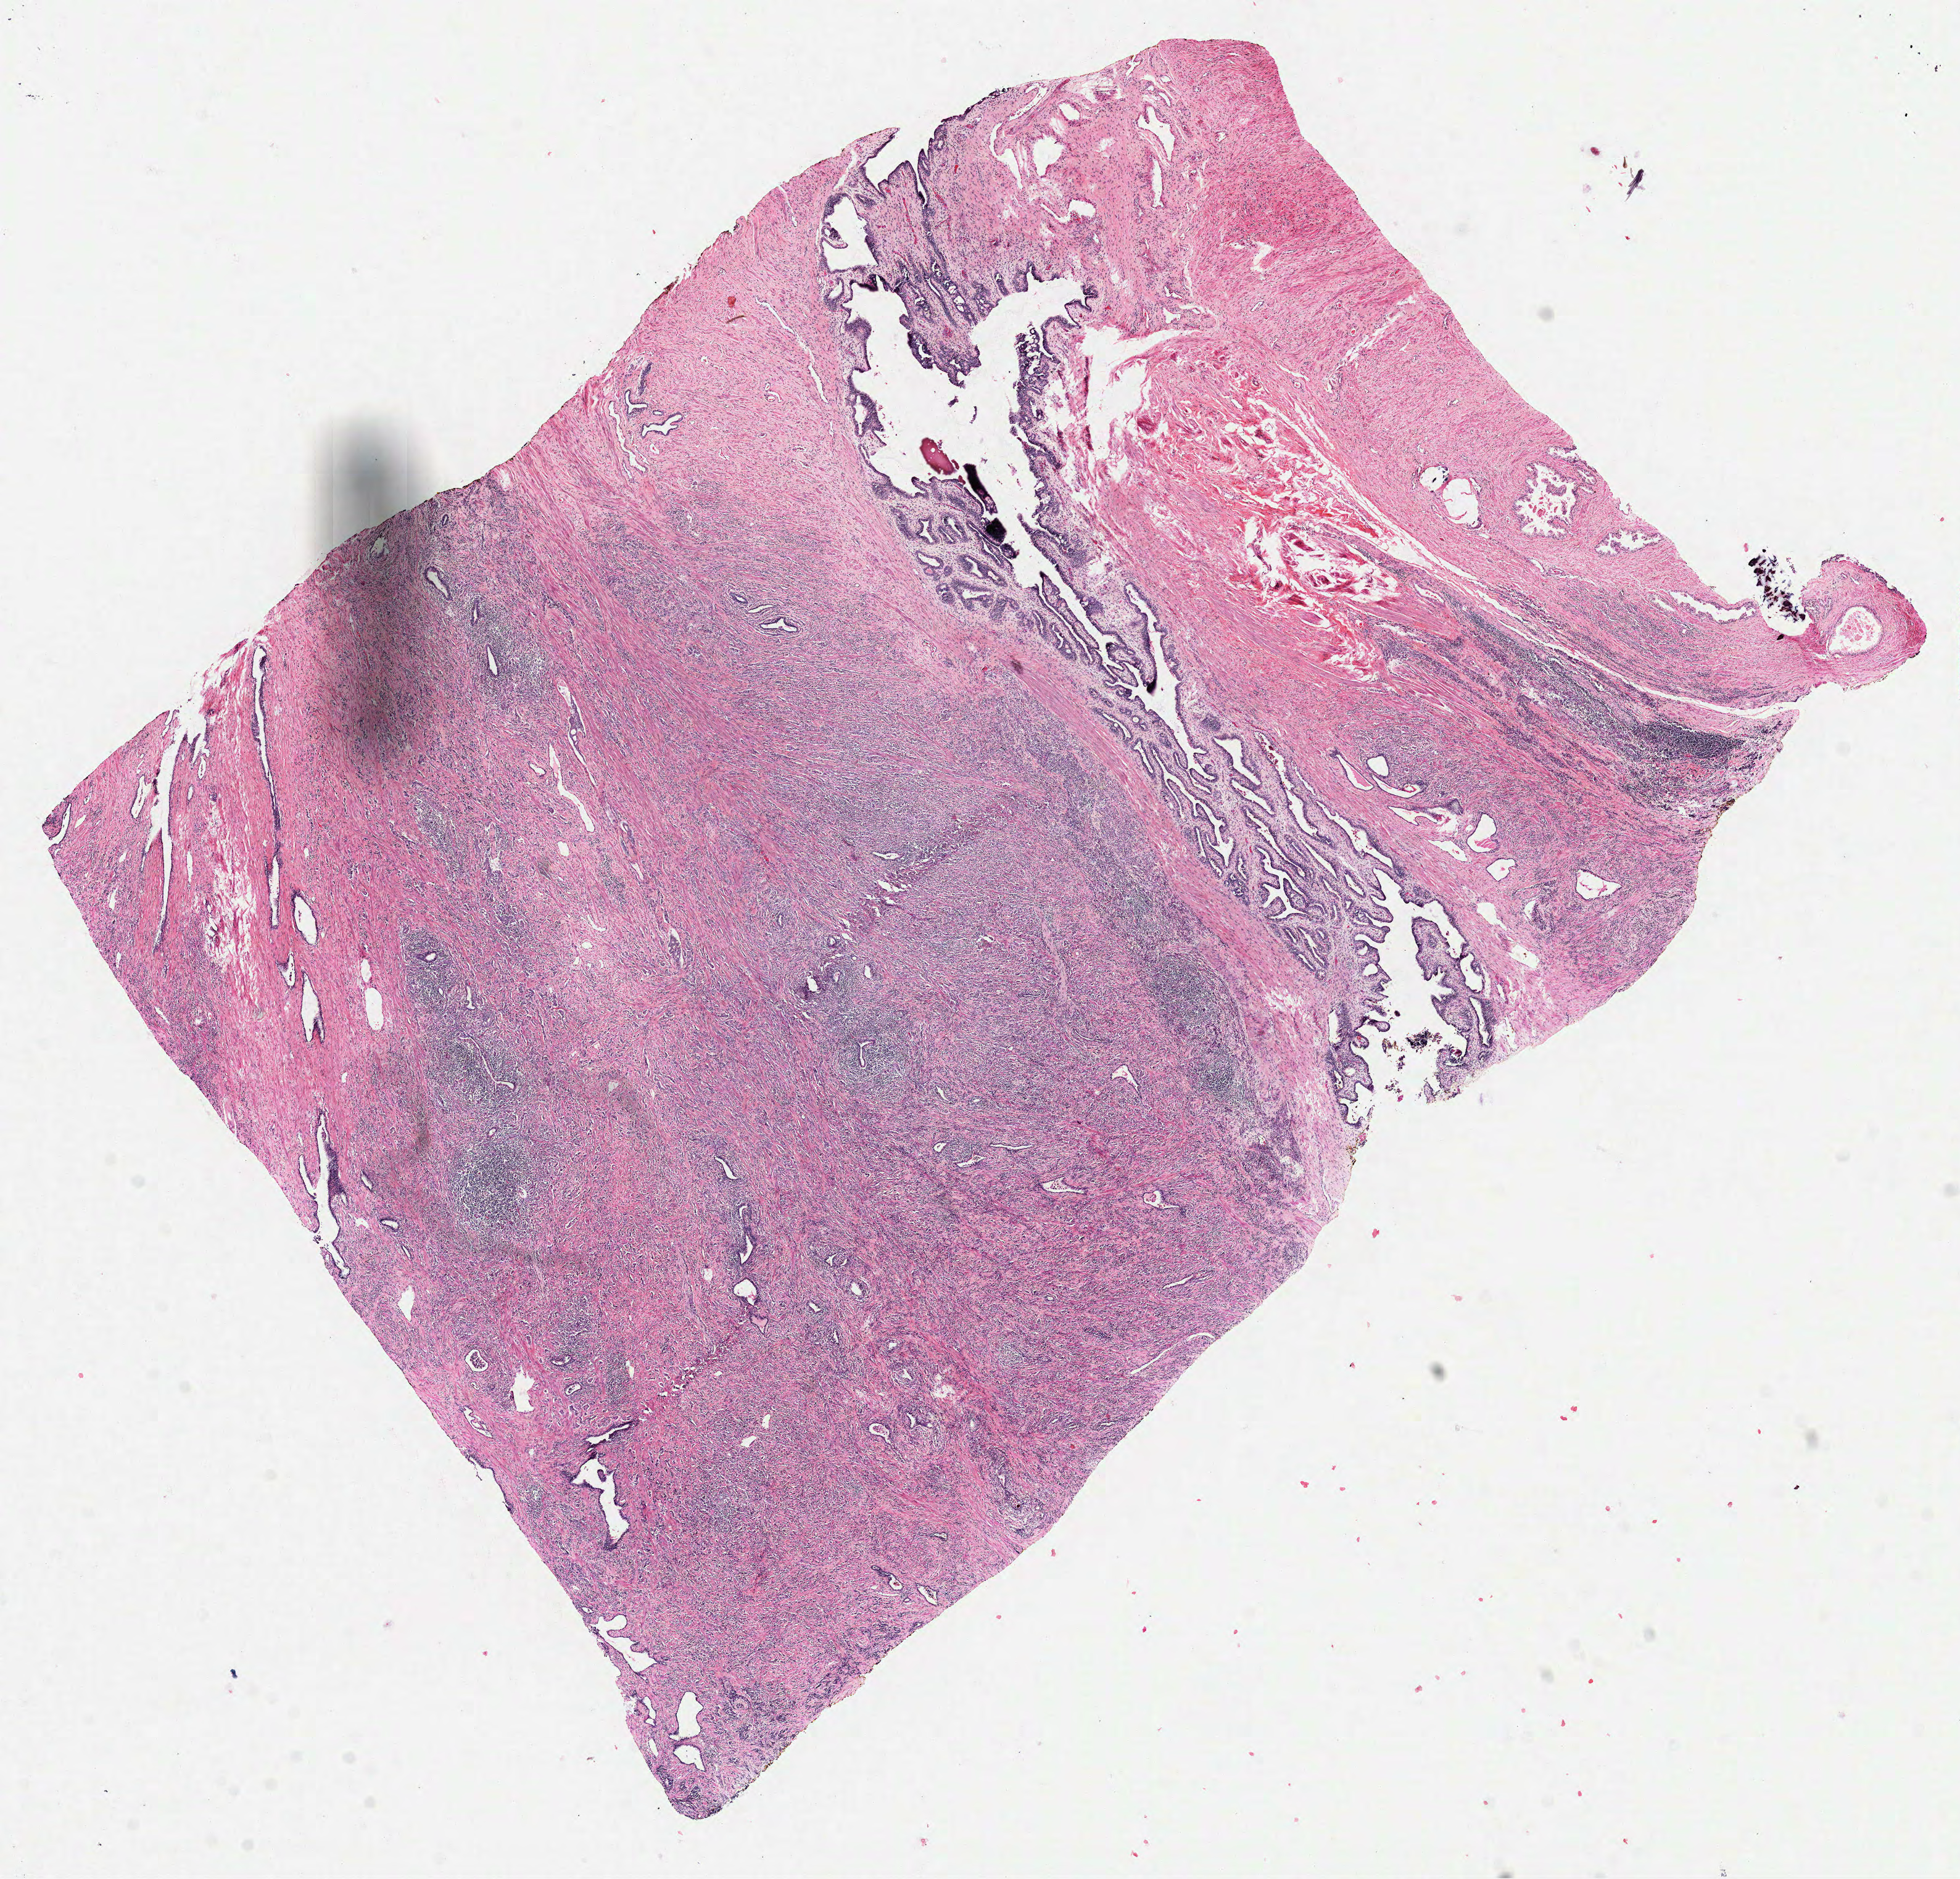
Whole-slide histology image, Hematoxylin and eosin (H&E) stained, shown as a low-resolution overview of the whole scanned area (about 12.8 x 12.3 mm, from a 40x scan), formalin-fixed paraffin-embedded (FFPE) diagnostic section, sample: primary tumour, prostate. Patient: male, age at initial diagnosis 56 years. Gleason score: 9 (5+4).
Pathologic diagnosis: Acinar cell carcinoma.